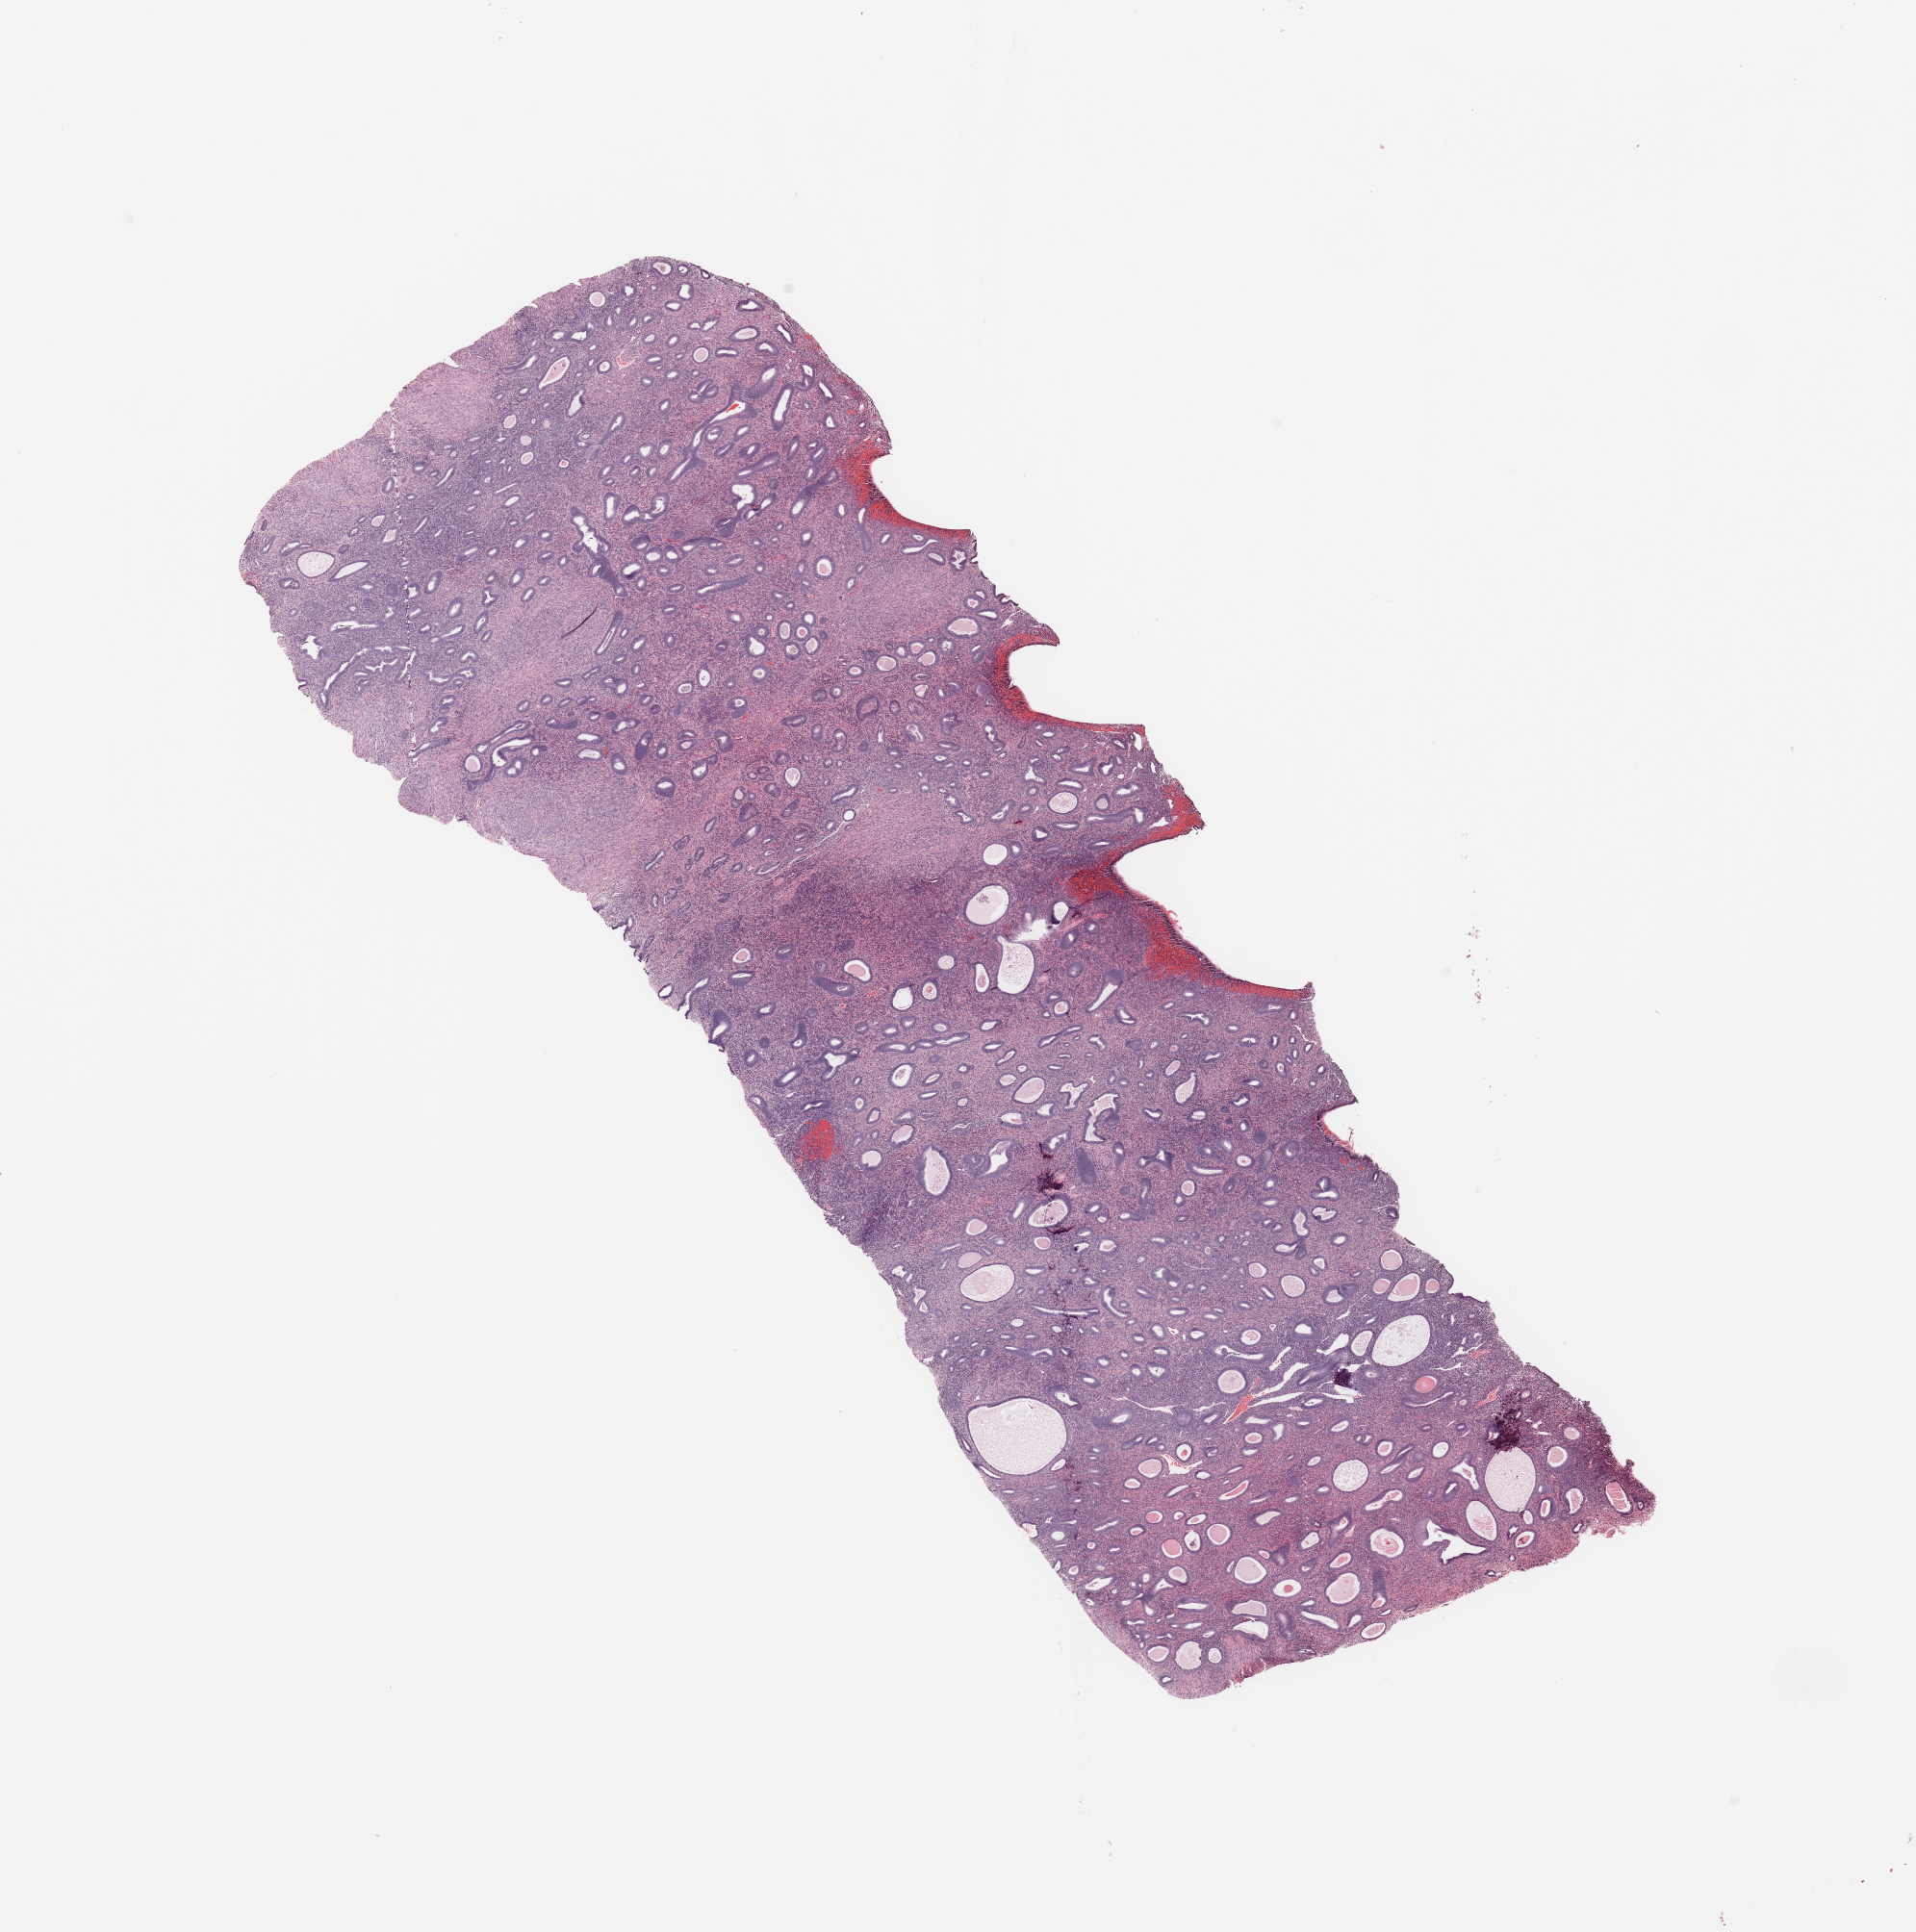
H&E whole-slide image — whole scanned area (about 15.8 x 15.9 mm, slide scanned at 20x) shown as a low-resolution overview. Uterus, normal (non-tumour) tissue. 62-year-old female patient.
• this section: normal (non-tumour) tissue from the same patient
• patient diagnosis: Endometrioid adenocarcinoma, NOS